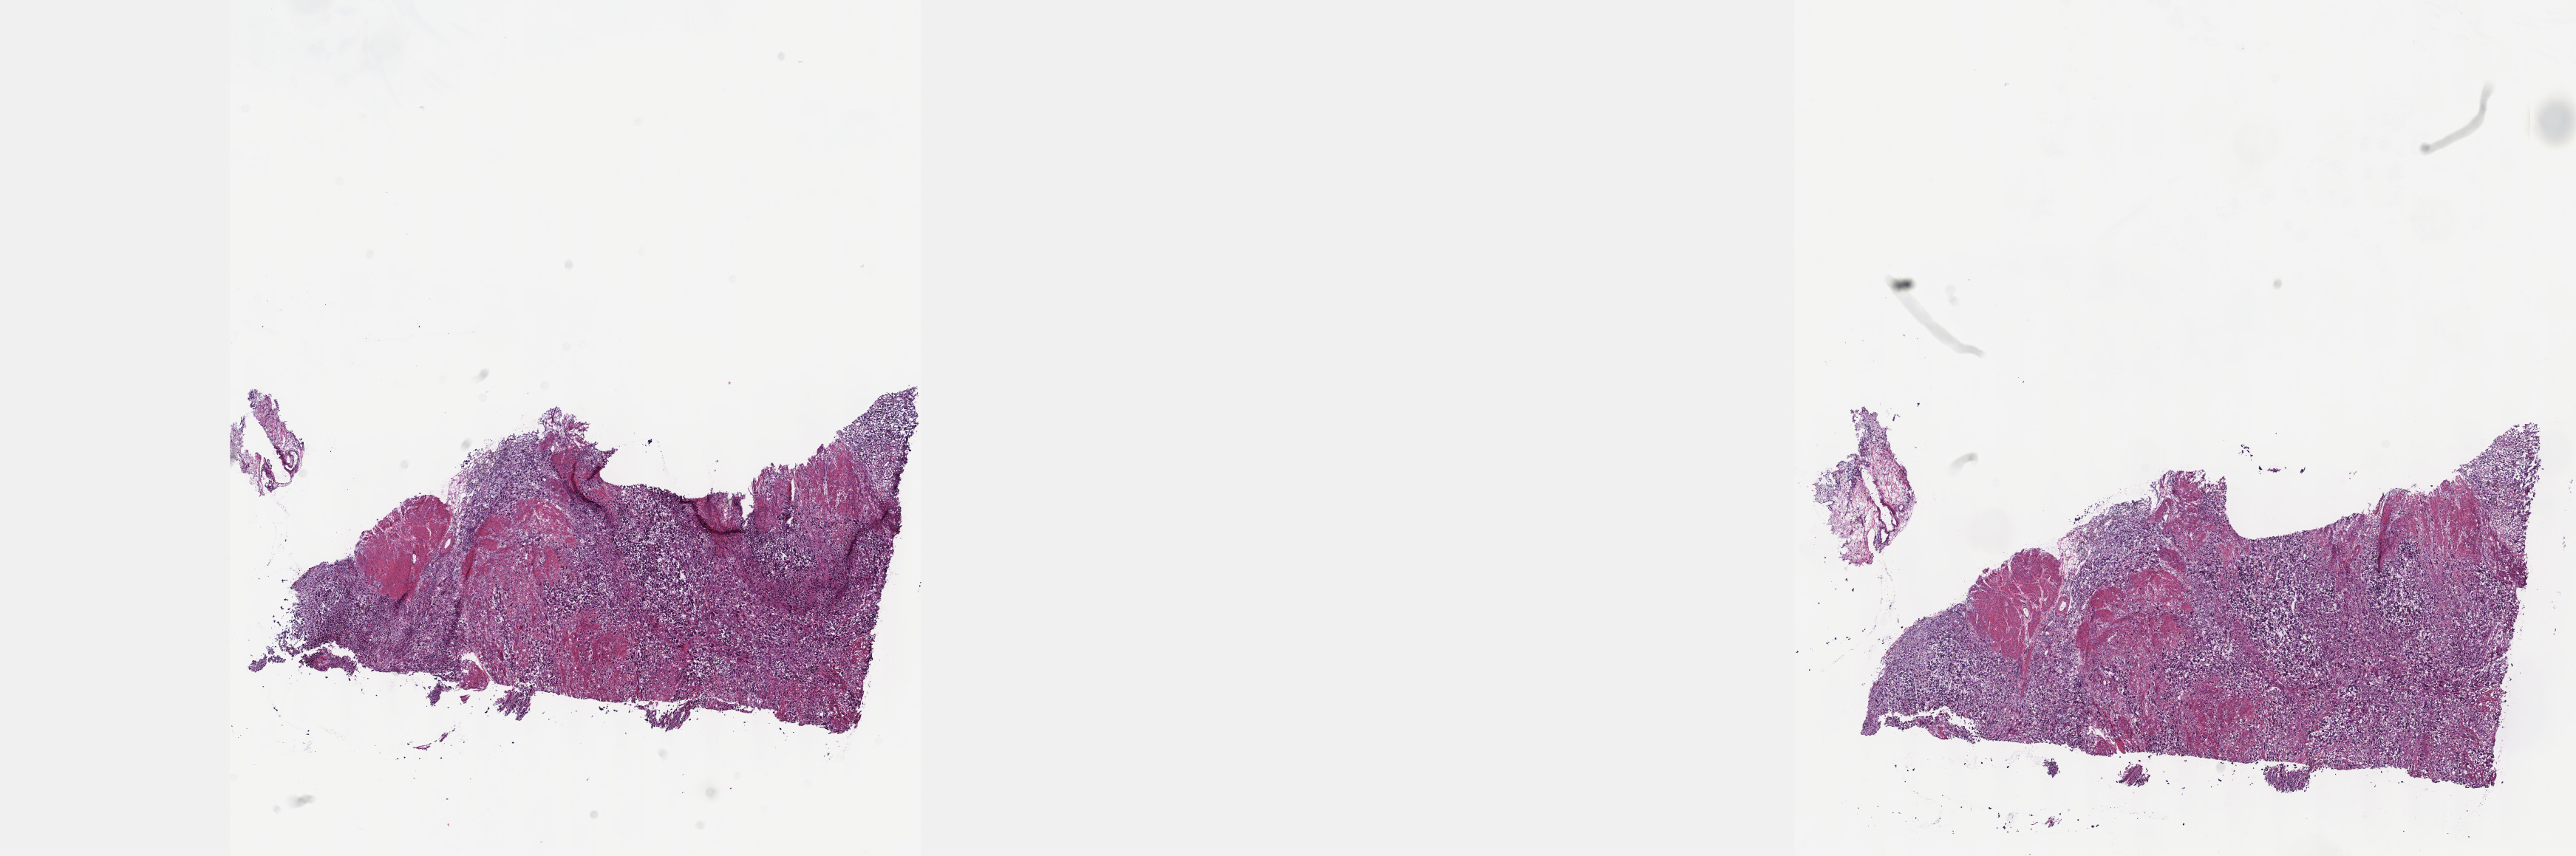
Digitized Hematoxylin and eosin (H&E) stained tissue section (whole slide), whole scanned area (about 28.2 x 9.4 mm, slide scanned at 40x) shown as a low-resolution overview. Frozen section. Sample: primary tumour, bladder. Patient: male, age at initial diagnosis 70 years. Histologic grade: high grade. Slide review estimates, as recorded: tumour cells 70%, tumour nuclei 80%, normal cells 0%, stromal cells 20%, necrosis 10%. Inflammatory infiltration, as recorded: lymphocyte infiltration 0%, monocyte infiltration 0%, neutrophil infiltration 0%.
TNM: T3a NX MX. AJCC pathologic stage: III (6th edition). Pathologic diagnosis: Transitional cell carcinoma (posterior wall of bladder).